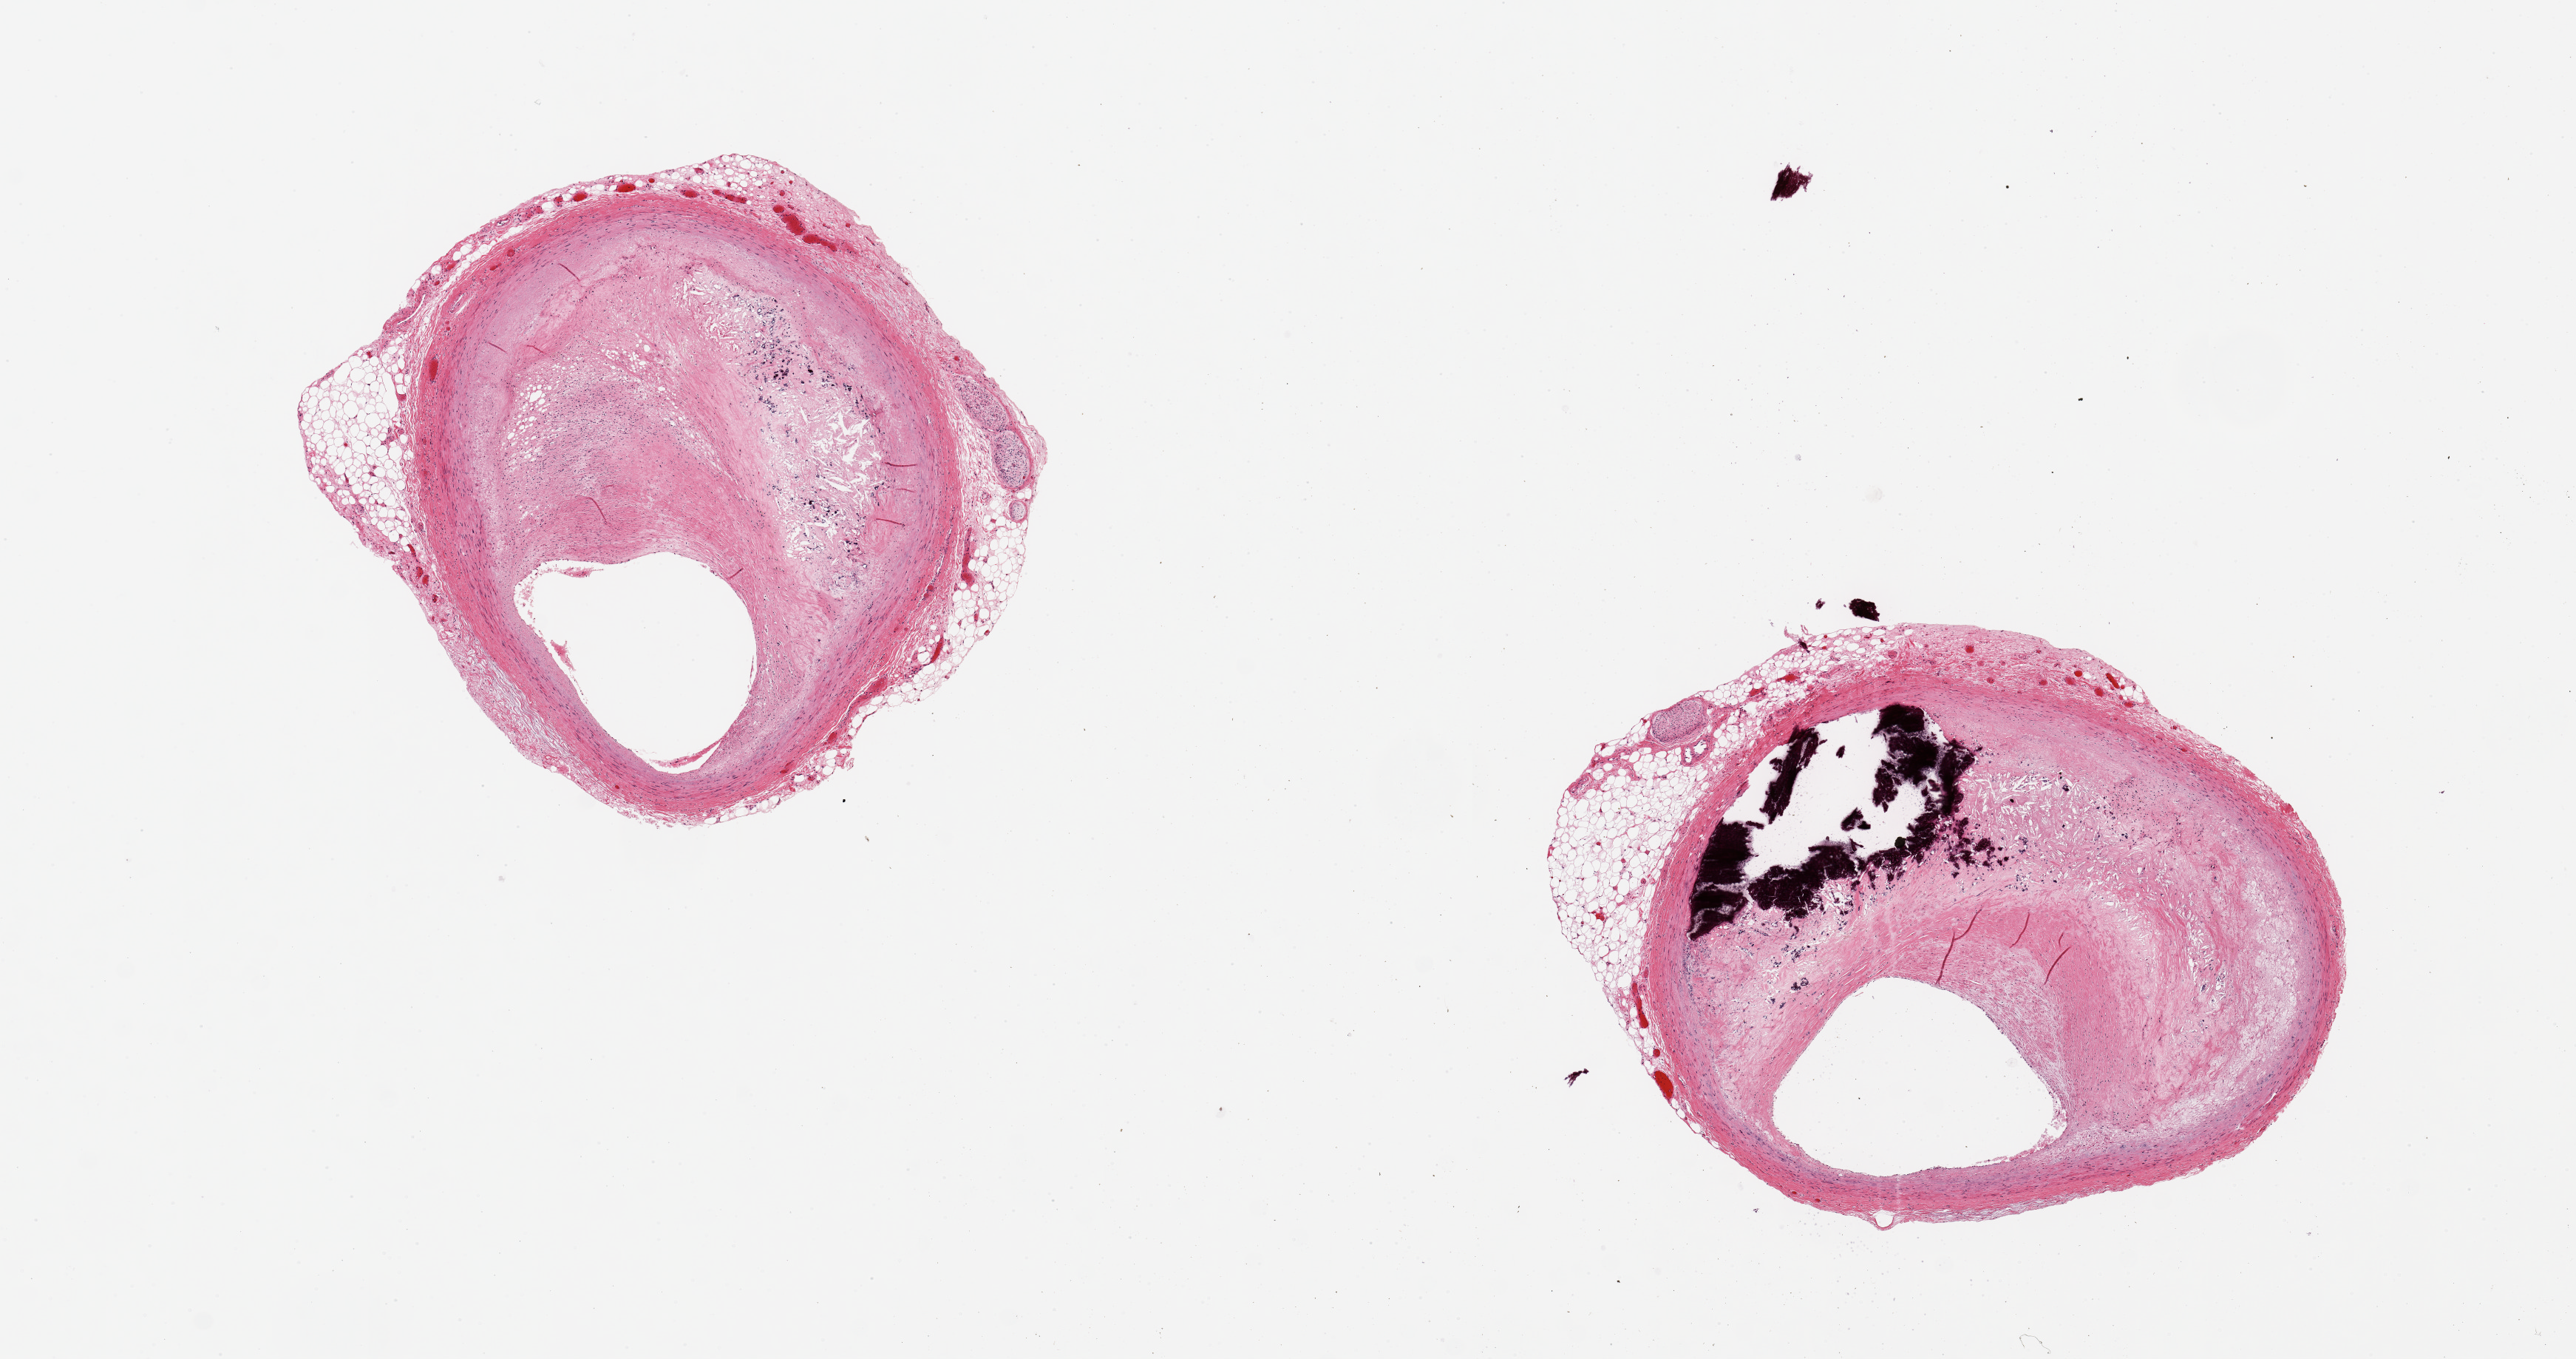
Digitized H&E-stained section, brightfield — whole scanned area (about 13.8 x 7.3 mm) shown as a low-resolution overview; PAXgene-fixed paraffin-embedded (PFPE) section; target tissue: coronary artery; tissue donor sample. Donor sex: female.
• reviewer comment on this tissue sample: 2 pieces, 3.7 & 3 mm arteries with extensive calcified atheromatous eccentric plaques occluding ~ 75% of the lumens; ~10% peripheral adipose